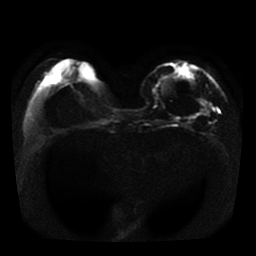
Breast MRI, one axial slice; position 13 of 41 along the scan axis; diffusion-weighted series; image 2 of 4 stored at this slice position (different b-values; order by instance number); 1.5 T; 5 mm slice thickness; 256 × 256 image matrix. Female patient.
Structures marked on this image (outlined manually by an expert reader):
- tumour on diffusion-weighted imaging: bounding box <187,100,214,118> (left, top, right, bottom; pixels)